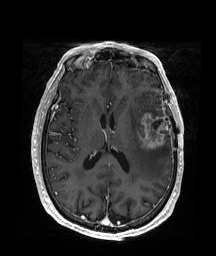
Brain MRI from a brain-tumour surgery series, one axial slice; position 86 of 176 along the scan axis; T1-weighted post-contrast; 1 mm slice thickness; 216 × 256 image matrix, field of view 219 × 260 mm. Case-level facts recorded for this patient, not image findings: histopathology: Glioblastoma; WHO grade: 4; IDH mutation: no; tumour location: Left Frontal.
Structures marked on this image (manually delineated by an expert):
- tumour: box from (x=136, y=112) to (x=168, y=150) px